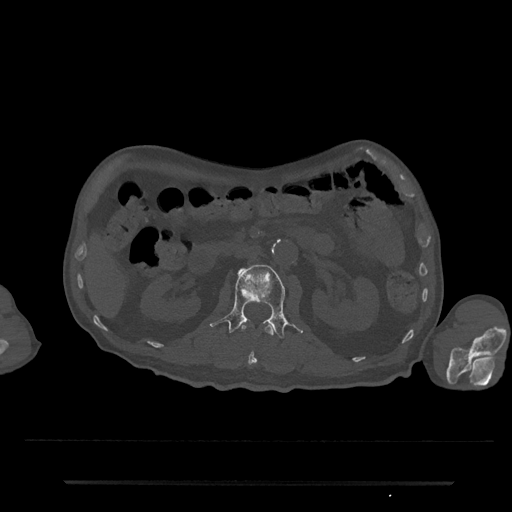
CT including the spine, one axial slice. Position 80 of 797 along the scan axis. 120 kVp. Bone window (W 1800 / L 400 HU). 0.5 mm slice thickness. 512 × 512 image matrix, field of view 427 × 427 mm. Patient: male, 74 years. From the clinical record (not read from this slice): primary cancer: prostate.
Outlined on this slice (semi-automatically segmented with operator editing):
- L1 vertebra: bounding box <240,323,274,366> (left, top, right, bottom; pixels)
- L2 vertebra: <210,264,302,339>